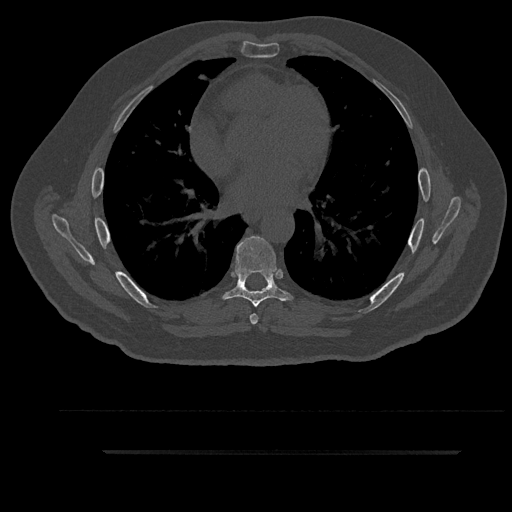
CT including the spine, one axial slice; position 534 of 797 along the scan axis; bone window (W 1800 / L 400 HU); 0.5 mm slice thickness; 512 × 512 image matrix, field of view 432 × 432 mm. Patient: male, 63 years. From the clinical record (not read from this slice): primary cancer: renal; vertebrae with lytic lesions (as recorded): T8.
Outlined on this slice (semi-automatic segmentation, software-assisted and operator-edited):
- T6 vertebra: box from (x=250, y=291) to (x=262, y=325) px
- T7 vertebra: (x=221, y=236)–(x=293, y=307)